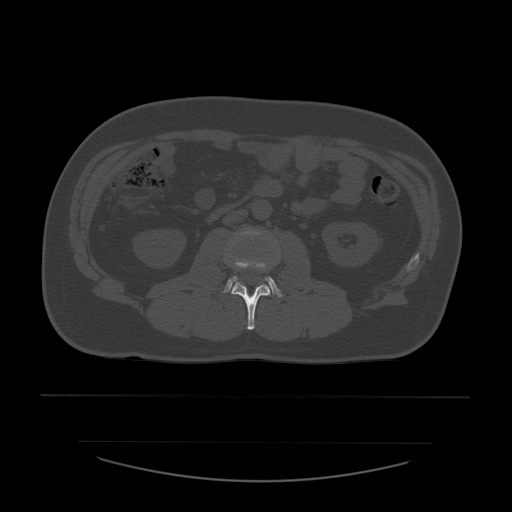
CT including the spine, one axial slice. Position 188 of 532 along the scan axis. Reconstruction kernel STANDARD. Bone window (W 1800 / L 400 HU). 1.25 mm slice thickness. 512 × 512 image matrix, field of view 441 × 441 mm. Patient age 44 years. From the clinical record (not read from this slice): primary cancer: soft tissue sarcoma.
Annotated regions visible in this slice (semi-automatic segmentation, software-assisted and operator-edited):
- L2 vertebra: bounding box (x1, y1, x2, y2) in pixels: (232, 282, 271, 330)
- L3 vertebra: (225, 233, 282, 297)